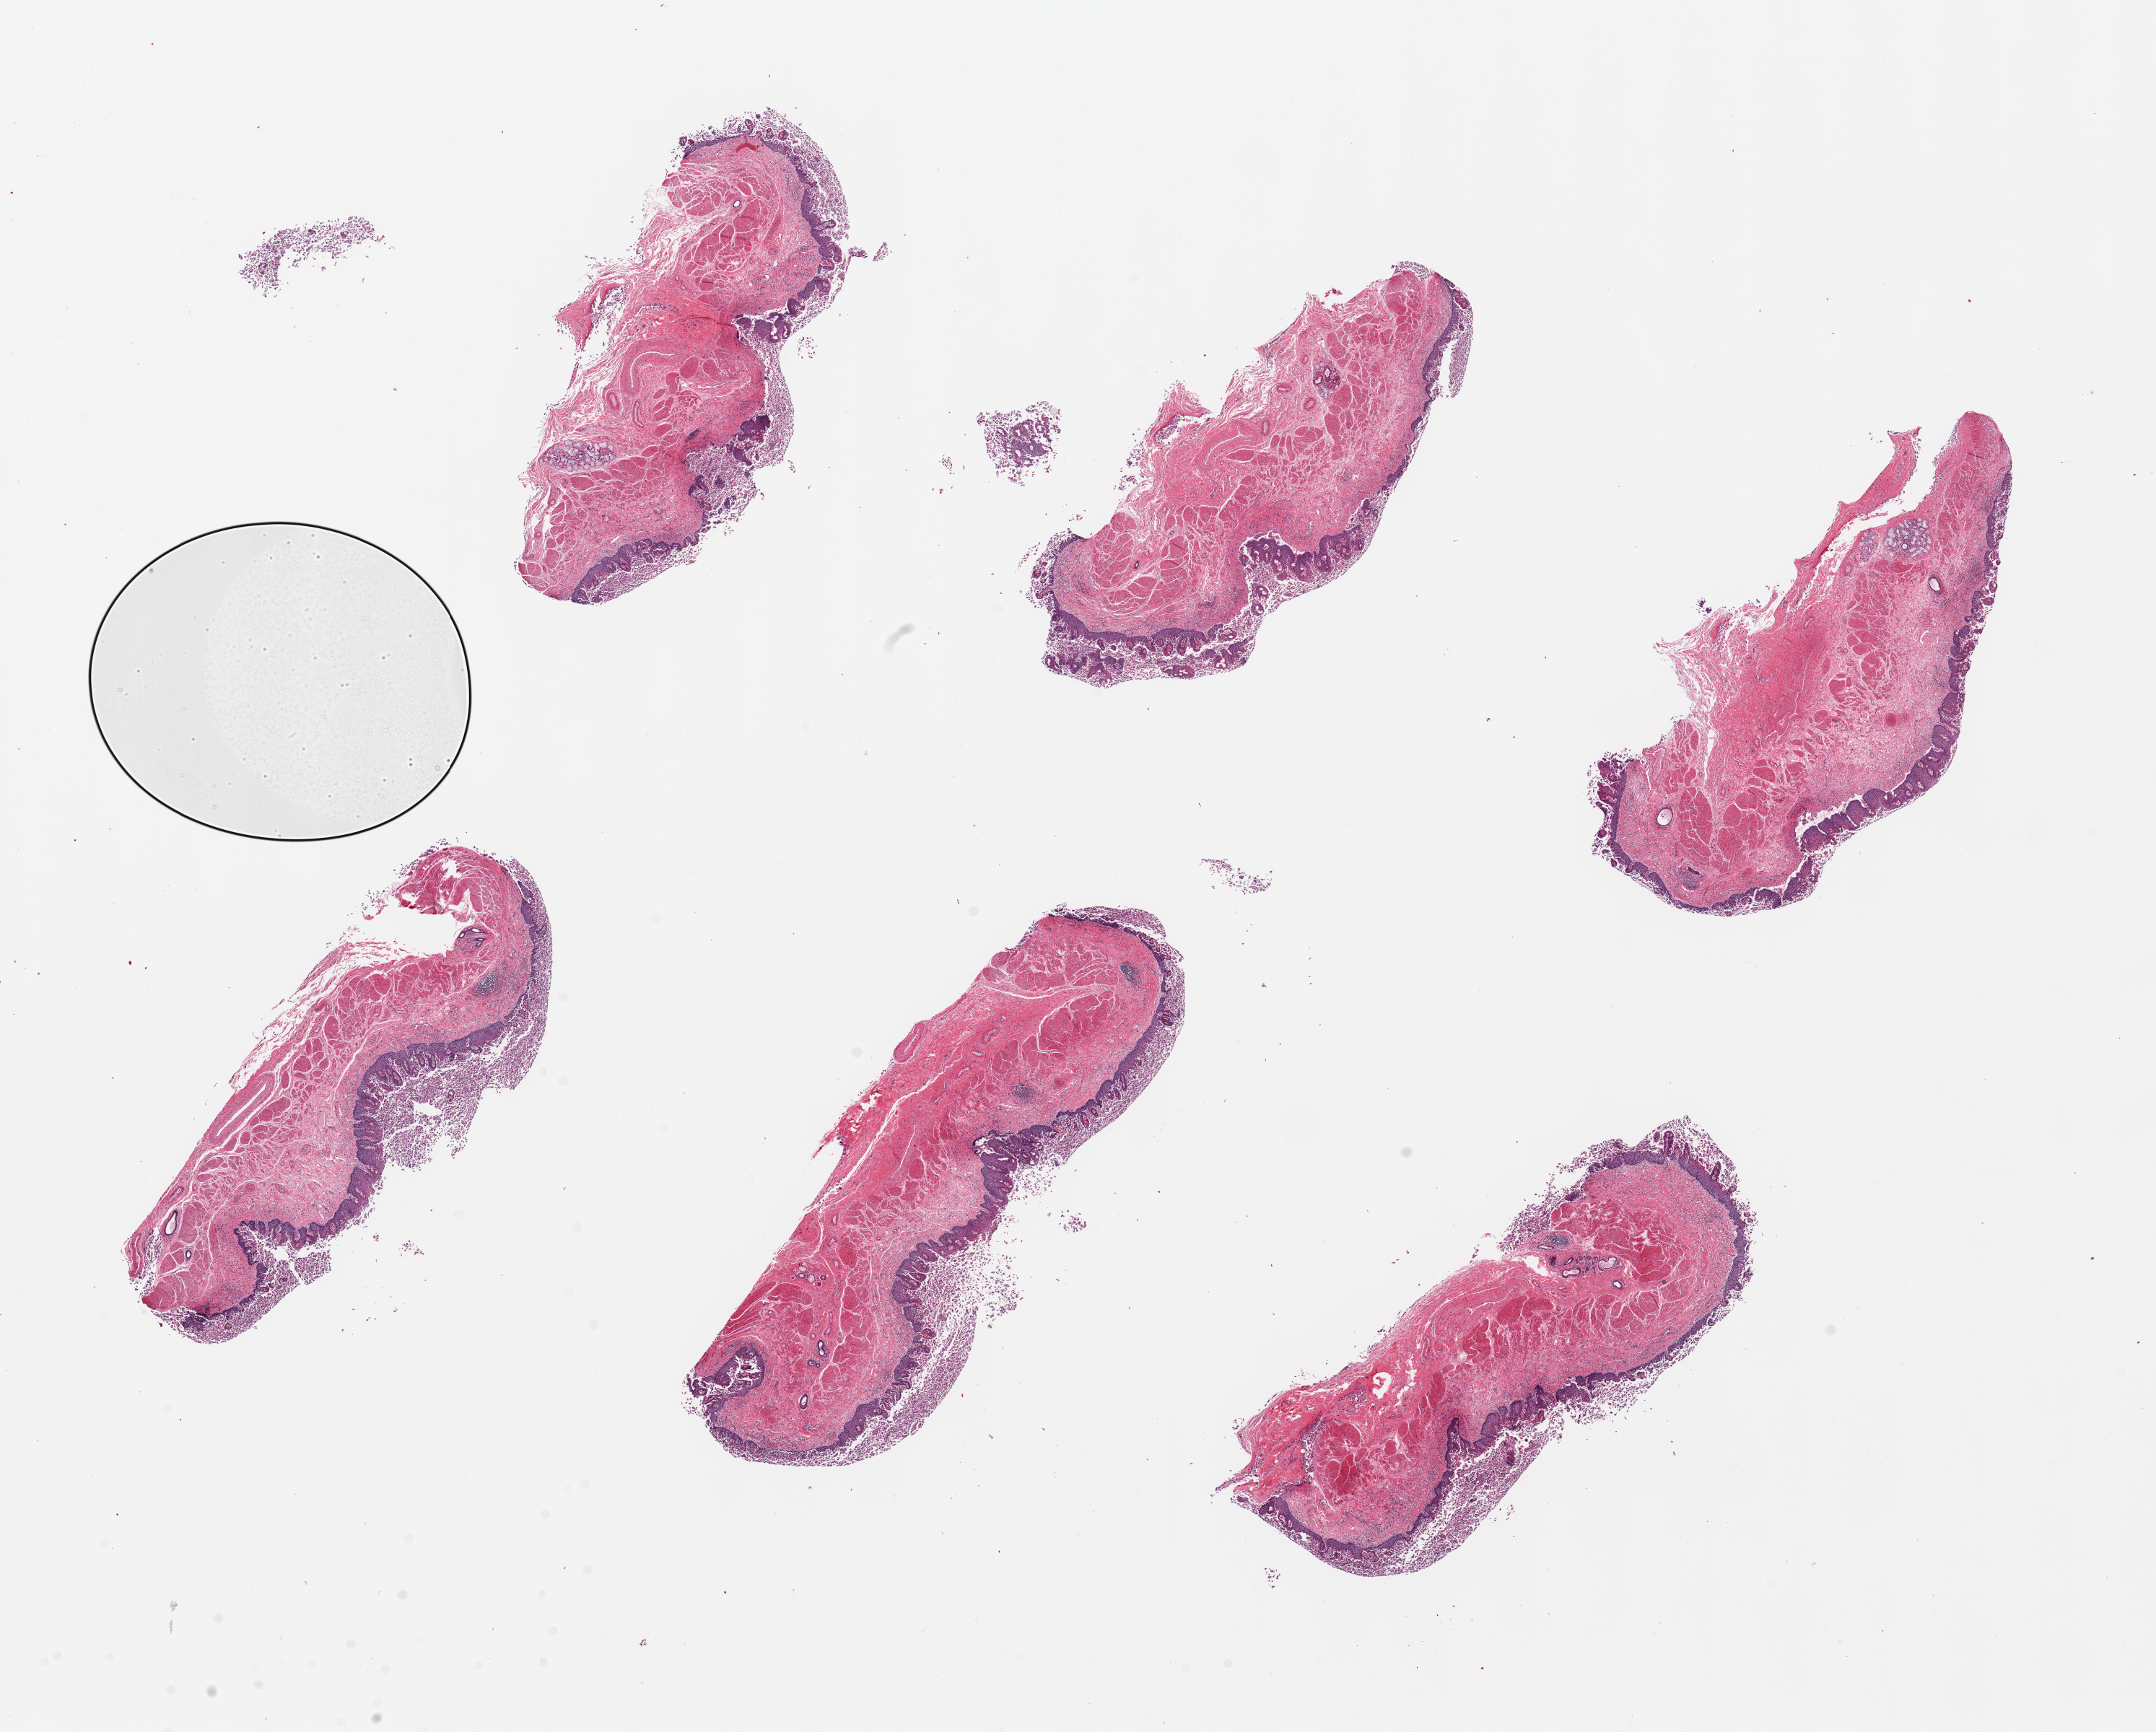
Whole-slide image, hematoxylin and eosin (H&E) stain — a low-resolution overview of the entire scanned area, about 23.6 x 19.0 mm, PAXgene-fixed paraffin-embedded (PFPE) section, target tissue: esophageal mucous membrane, donor tissue sample. Male donor.
* pathologist's review note for this sample: 6 pieces, up to 7x3mm; Prominent superficial sloughing of squamous lining